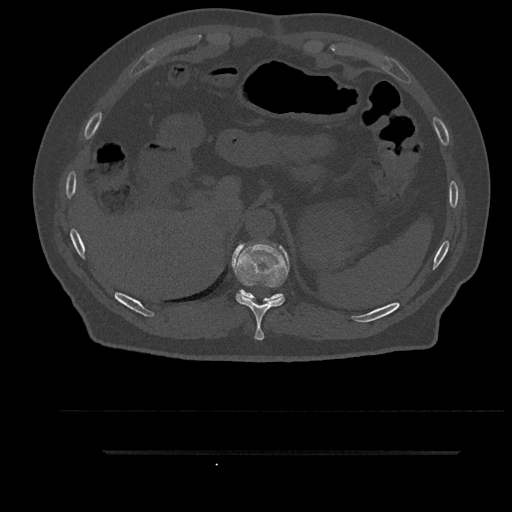
CT including the spine, one axial slice. Slice 344 of 797 in the series (ordered by position). Reconstruction kernel Br40s/3. 120 kVp. Bone window (W 1800 / L 400 HU). 0.5 mm slice thickness. 512 × 512 image matrix, field of view 432 × 432 mm. Patient: male, 63 years. Case-level facts recorded for this patient, not image findings: primary cancer: renal.
Structures marked on this image (semi-automatic segmentation, software-assisted and operator-edited):
- T10 vertebra: box from (x=232, y=241) to (x=289, y=341) px
- T11 vertebra: (x=237, y=290)–(x=283, y=302)